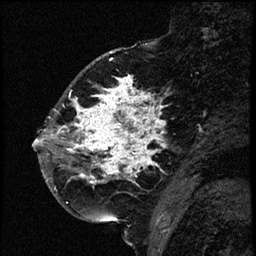
Breast MRI (dynamic contrast-enhanced), one sagittal slice; slice 24 of 66 in the series (ordered by position); dynamic contrast-enhanced study with each time point stored as its own series, time point 2 of 3 at this slice position (early post-contrast, ordered by acquisition time); 1.5 T; TE 4.2 ms, TR 17.6 ms; 2 mm slice thickness; 256 × 256 image matrix, field of view 200 × 200 mm. Female patient. From the clinical record (not read from this slice): setting: breast cancer imaged before/during neoadjuvant chemotherapy; receptor status: HER2-positive.
Outlined on this slice (semi-automatic segmentation, software-assisted and operator-edited):
- analysis volume of interest (the breast-tissue region the enhancement analysis was run in; not a lesion): bounding box (x1, y1, x2, y2) in pixels: (52, 69, 177, 209)
- tumour enhancement mask (voxels above the 100 % enhancement threshold inside the analysis volume of interest): (52, 76, 164, 185)